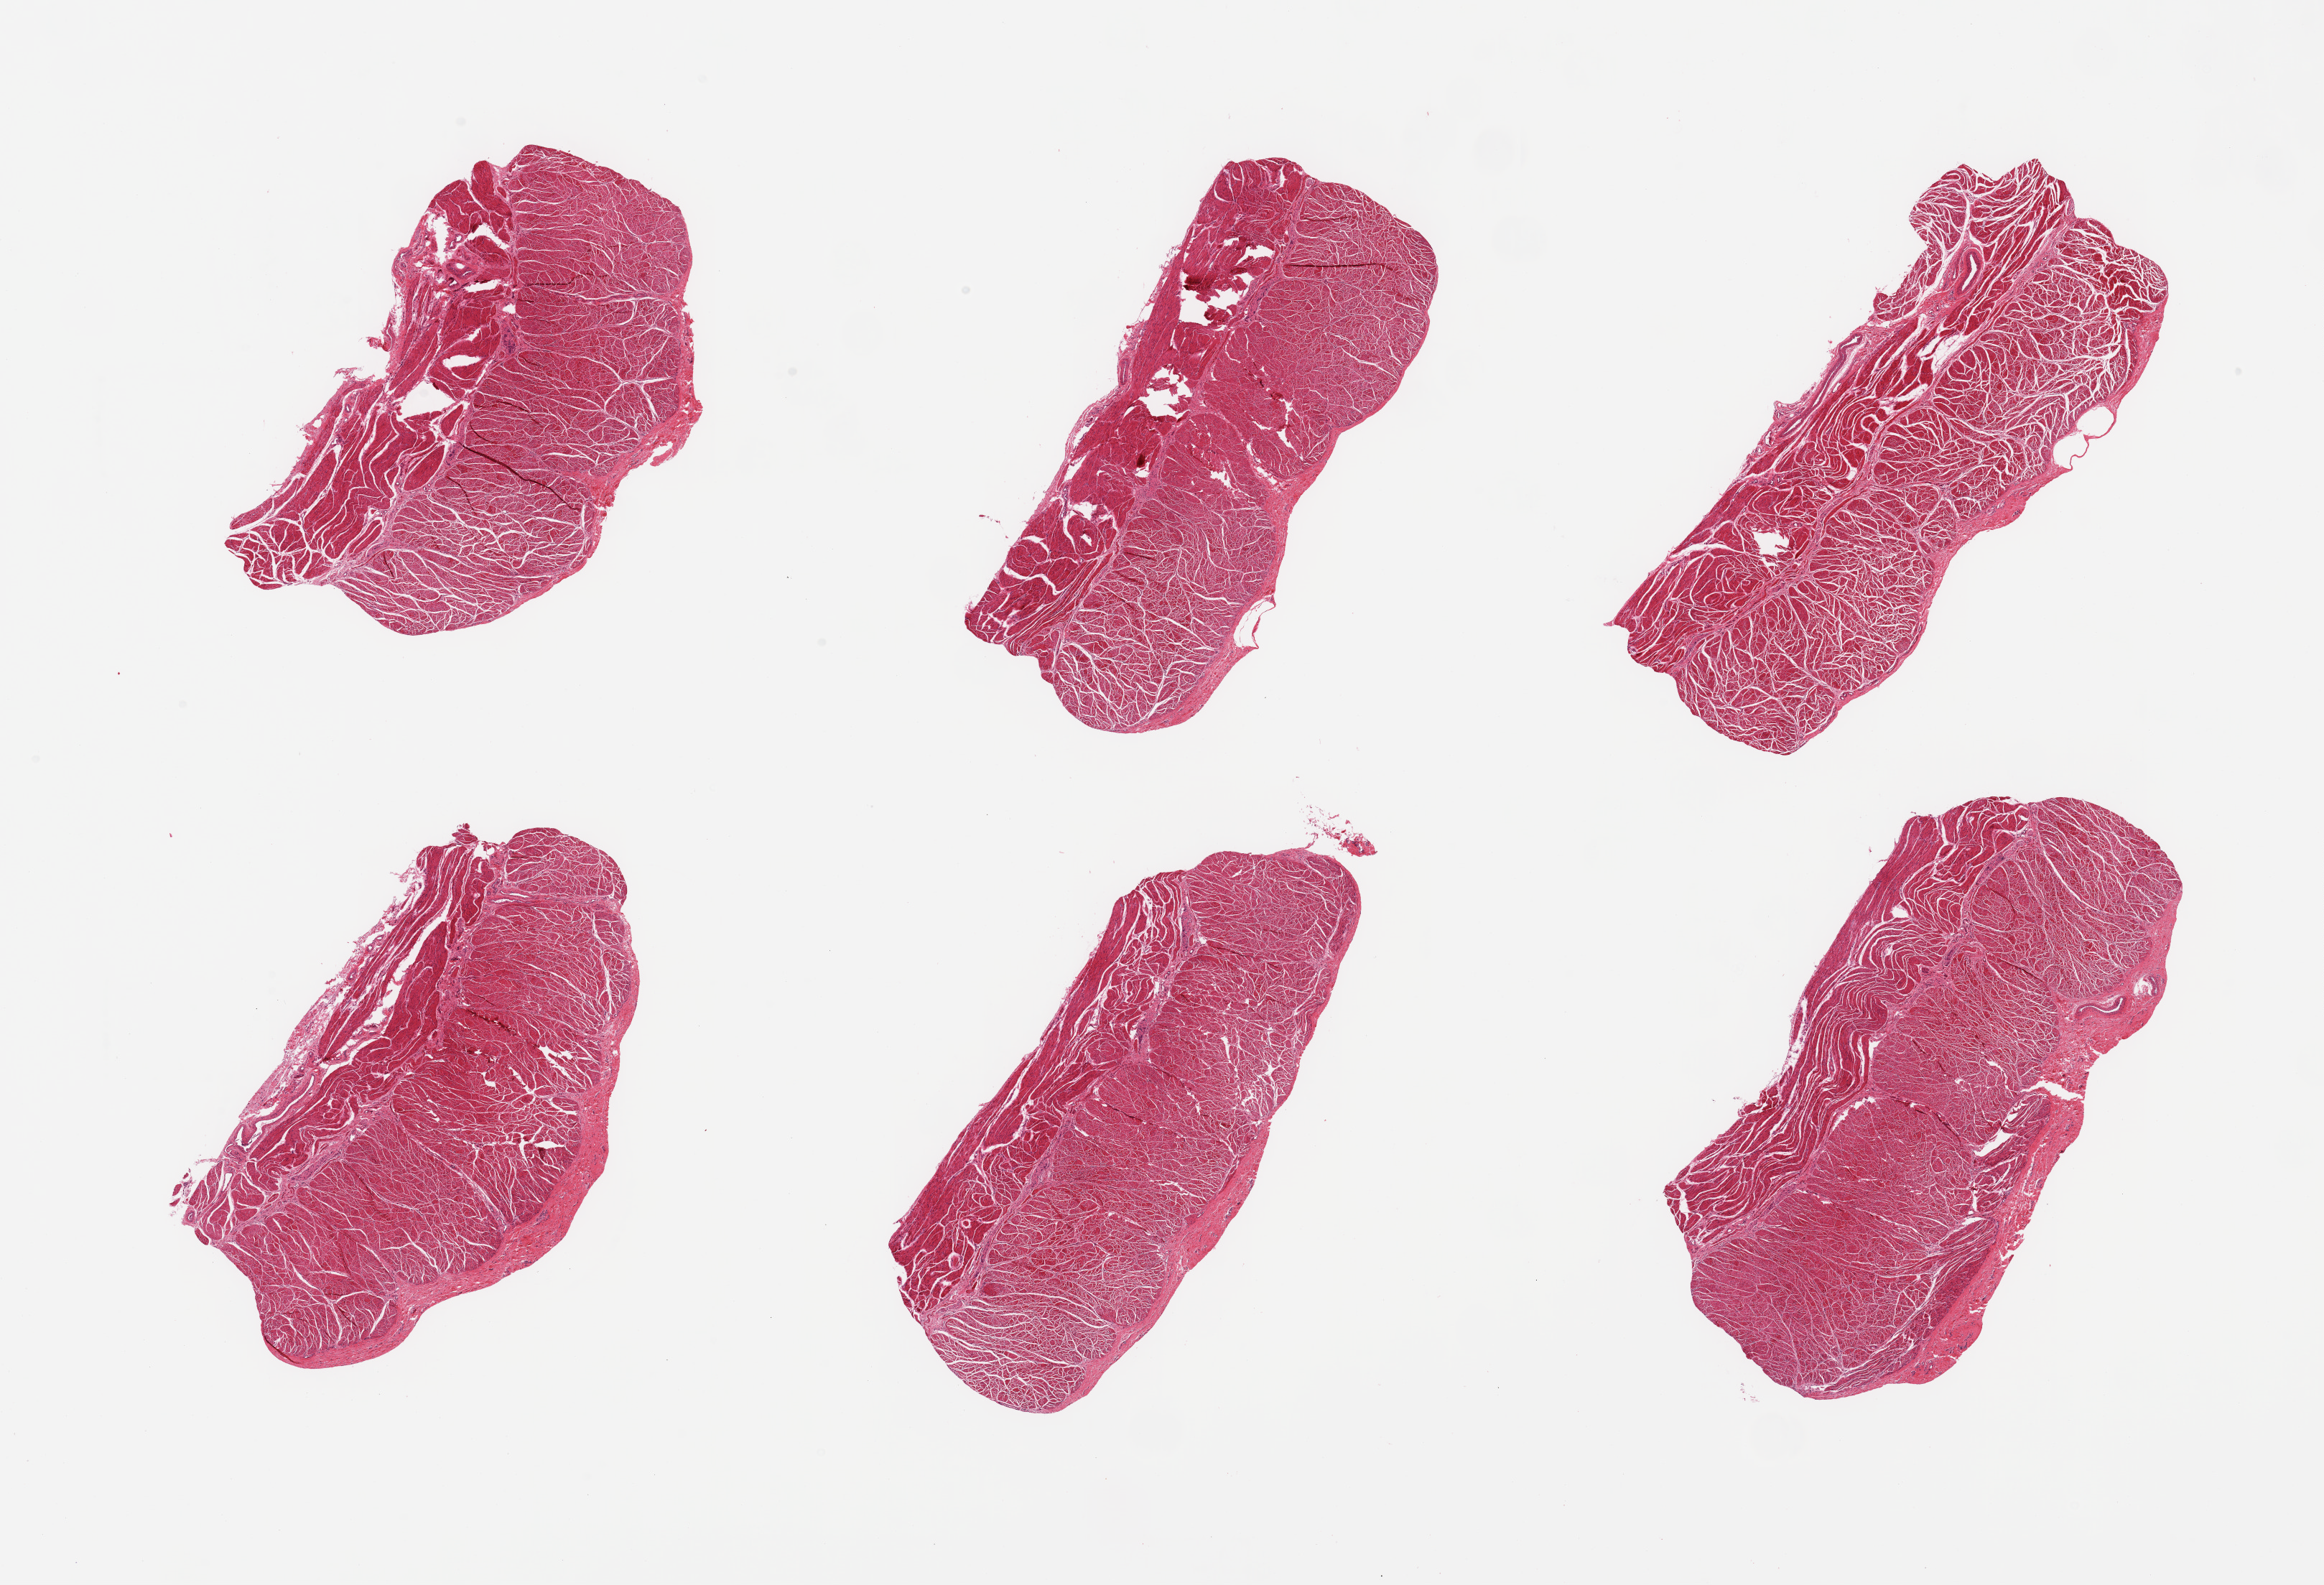
Haematoxylin and eosin whole-slide image, whole scanned area (about 25.6 x 17.5 mm, slide scanned at 20x) shown as a low-resolution overview, PAXgene-fixed paraffin-embedded (PFPE) section, section of esophageal muscle (target tissue), tissue donor sample.
Review note (as recorded): 6 pieces, confirmed target muscularis.